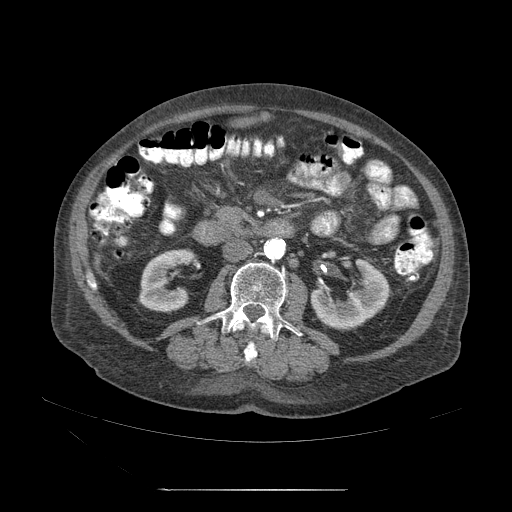
Contrast-enhanced abdominal CT (liver protocol), one axial slice. Position 1 of 71 along the scan axis. Reconstruction kernel STANDARD. 120 kVp. Soft-tissue window (W 400 / L 40 HU). 2.5 mm slice thickness. 512 × 512 image matrix, field of view 440 × 440 mm. Case-level facts recorded for this patient, not image findings: diagnosis: hepatocellular carcinoma (patient treated with transarterial chemoembolisation; whether this scan precedes or follows treatment is not stated here); TNM stage (as recorded): Stage-II; Child-Pugh class: A; tumour nodularity: multinodular; tumour size: 1 cm.
Structures marked on this image (semi-automatic segmentation, software-assisted and operator-edited):
- abdominal aorta: bounding box <264,238,286,260> (left, top, right, bottom; pixels)